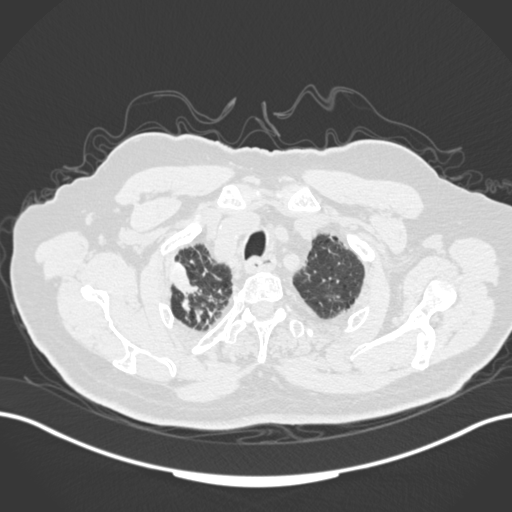
Chest CT, one axial slice. Slice 152 of 205 in the series (ordered by position). Reconstruction kernel B30f. 120 kVp. Lung window (W 1500 / L -600 HU). 1 mm slice thickness. 512 × 512 image matrix. Male patient, age 72 years. From the clinical record (not read from this slice): clinical TNM (as recorded): T1a N0 M0.
Annotated regions visible in this slice (bounding box drawn by a radiologist):
- lung tumour (recorded histology: squamous cell carcinoma): bounding box [x1, y1, x2, y2] px = [165, 256, 205, 320]